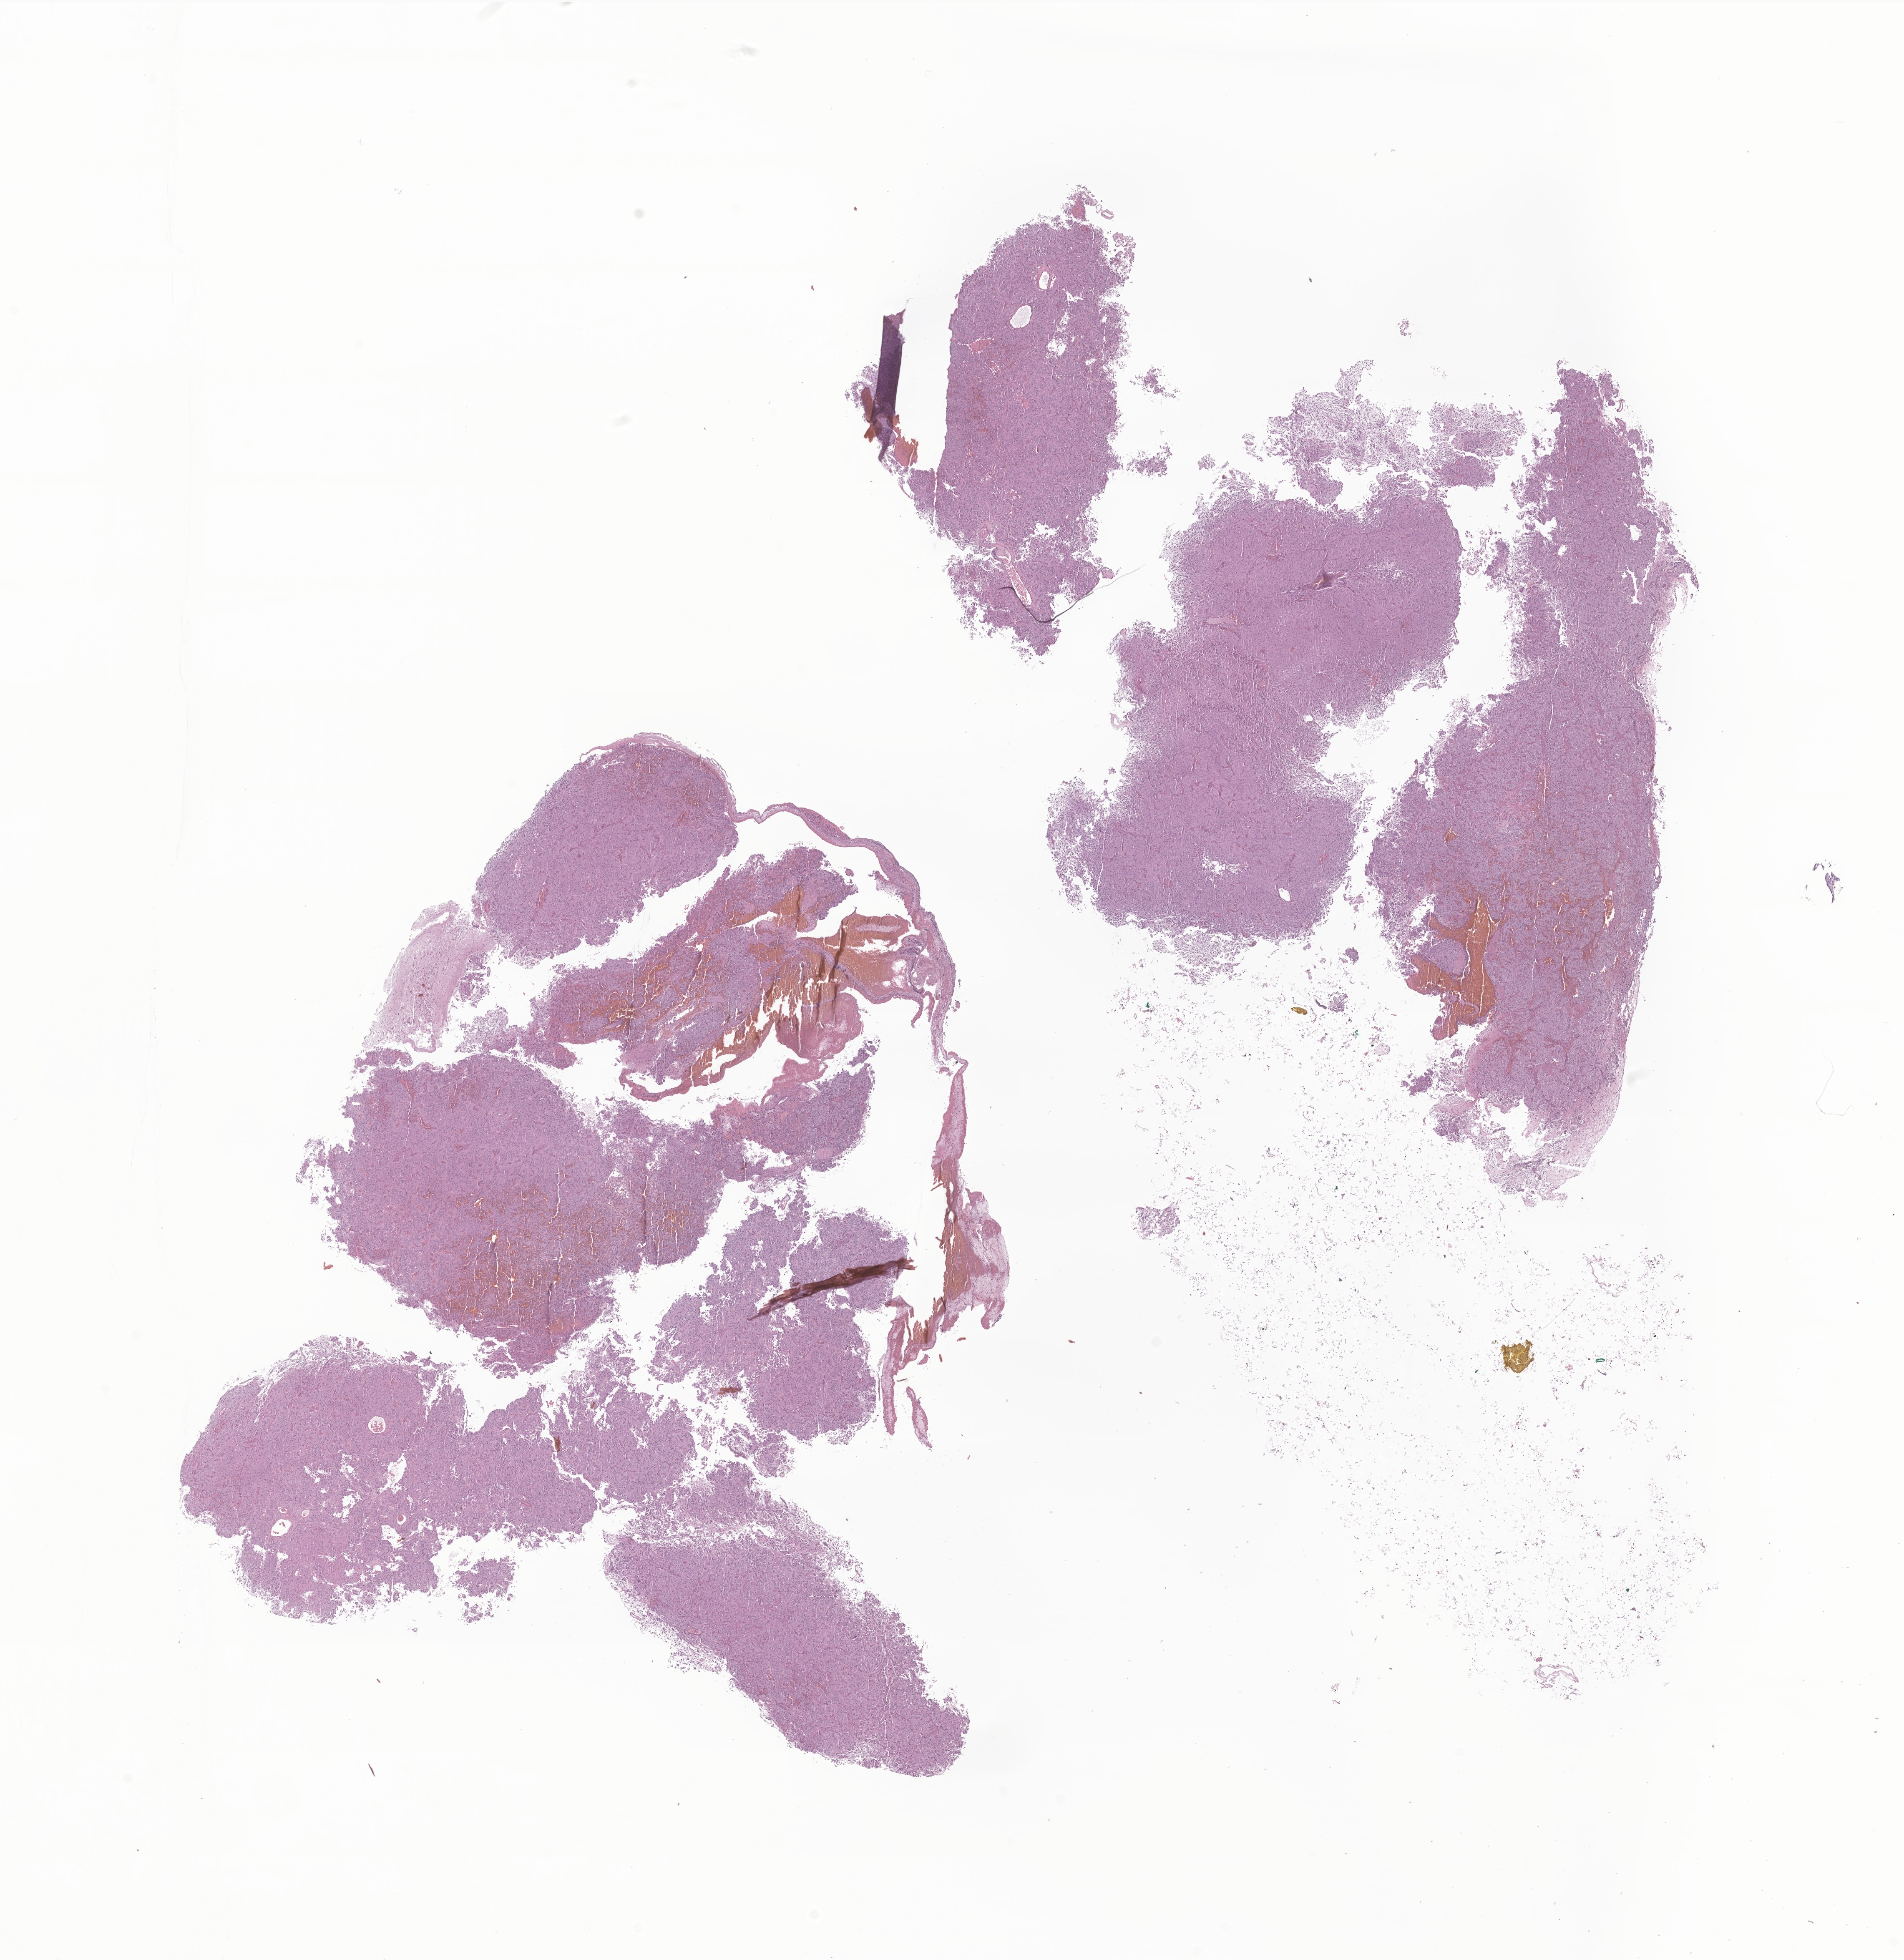
H&E whole-slide image of tumor tissue from the cerebral ventricle — a low-resolution overview of the entire scanned area, about 19.2 x 19.8 mm. FFPE section. Patient male; age 111 months.
Diagnosis: Subependymal giant cell astrocytoma.